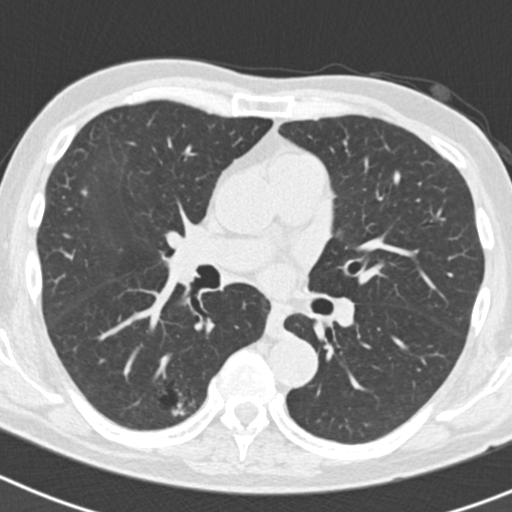
Low-dose screening chest CT, axial slice; second annual screen; lung window (W 1500 / L -600 HU); 2 mm slice thickness; 120 kVp; slice 81 of 186 in the series; 512 × 512 image matrix. Male participant, aged 70 years at enrolment. Current smoker at enrolment.
Lesion marked by an expert reader, bounding box [x1, y1, x2, y2] px = [131, 371, 200, 432]. The screening reader recorded 5 non-calcified nodules or masses ≥4 mm on this exam (right lower lobe, right lower lobe, right upper lobe, right upper lobe, left upper lobe); which of them this box marks is not recorded. Official screen result: positive, other. Participant outcome: lung cancer diagnosed 622 days after this screen (after the third annual screen) — bronchiolo-alveolar adenocarcinoma, NOS, right lower lobe, poorly differentiated (G3), stage IB (AJCC 6th edition), 30 mm at pathology.